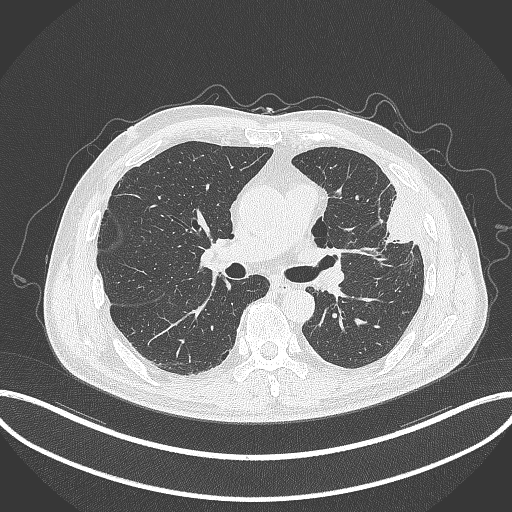
Chest CT, one axial slice. Position 190 of 382 along the scan axis. Reconstruction kernel B70f. Lung window (W 1500 / L -600 HU). 1 mm slice thickness. 512 × 512 image matrix, field of view 415 × 415 mm. Patient: male, 64 years. From the clinical record (not read from this slice): clinical TNM (as recorded): T4 N1 M0.
Annotated regions visible in this slice (rectangle marked by the reading radiologist):
- lung tumour (recorded histology: adenocarcinoma): bounding box (x1, y1, x2, y2) in pixels: (369, 191, 419, 253)